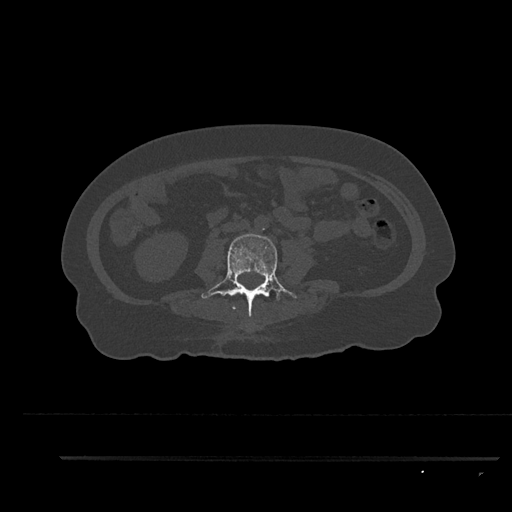
CT including the spine, one axial slice. Position 89 of 797 along the scan axis. Reconstruction kernel Br40s/3. 120 kVp. Bone window (W 1800 / L 400 HU). 512 × 512 image matrix, field of view 408 × 408 mm. Patient: female, 44 years. From the clinical record (not read from this slice): primary cancer: renal; vertebrae with lytic lesions (as recorded): L1.
Outlined on this slice (semi-automatic segmentation, software-assisted and operator-edited):
- L2 vertebra: bounding box [x1, y1, x2, y2] px = [233, 307, 236, 309]
- L3 vertebra: [201, 233, 297, 317]